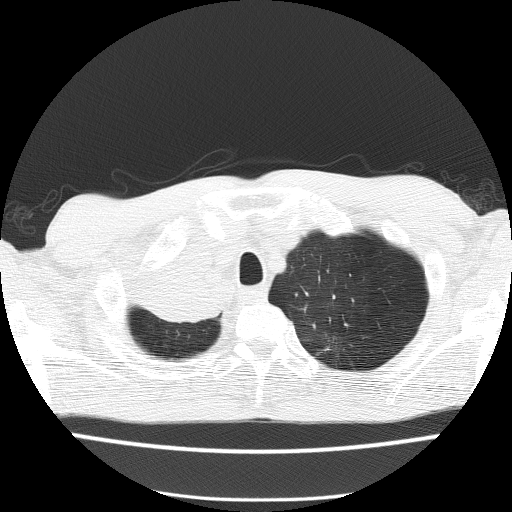
Low-dose screening chest CT, one axial slice; position 128 of 150 along the scan axis; 120 kVp; lung window (W 1500 / L -600 HU); 512 × 512 image matrix.
Annotated regions visible in this slice (outlined manually by an expert reader):
- lesion 1 (tumor, hilum of right lung): bounding box <136,253,229,320> (left, top, right, bottom; pixels)